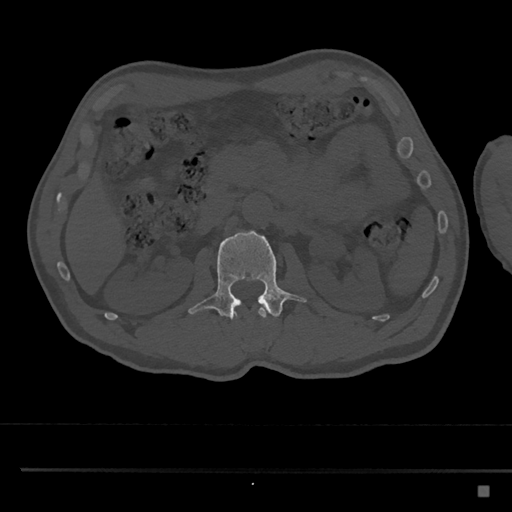
CT including the spine, one axial slice; slice 773 of 797 in the series (ordered by position); reconstruction kernel Br40s/3; 120 kVp; bone window (W 1800 / L 400 HU); 512 × 512 image matrix, field of view 391 × 391 mm. Patient: male, 59 years. Case-level facts recorded for this patient, not image findings: primary cancer: prostate.
Structures marked on this image (semi-automatic segmentation, software-assisted and operator-edited):
- L1 vertebra: bounding box (x1, y1, x2, y2) in pixels: (231, 308, 267, 318)
- L2 vertebra: (188, 230, 308, 319)